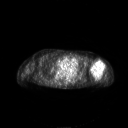
FDG PET of an extremity soft-tissue mass (from a PET/CT study), one axial slice. Slice 169 of 267 in the series (ordered by position). 128 × 128 image matrix, field of view 700 × 700 mm. Patient: female, 83 years. From the clinical record (not read from this slice): histological type: pleiomorphic leiomyosarcoma; grade: high; site of the primary tumour: left biceps.
Structures marked on this image (expert contour drawn on MRI and transferred to this co-registered scan by the dataset authors):
- gross tumour volume including surrounding oedema: bounding box (x1, y1, x2, y2) in pixels: (90, 59, 105, 77)
- gross tumour volume (mass): (90, 59, 104, 77)